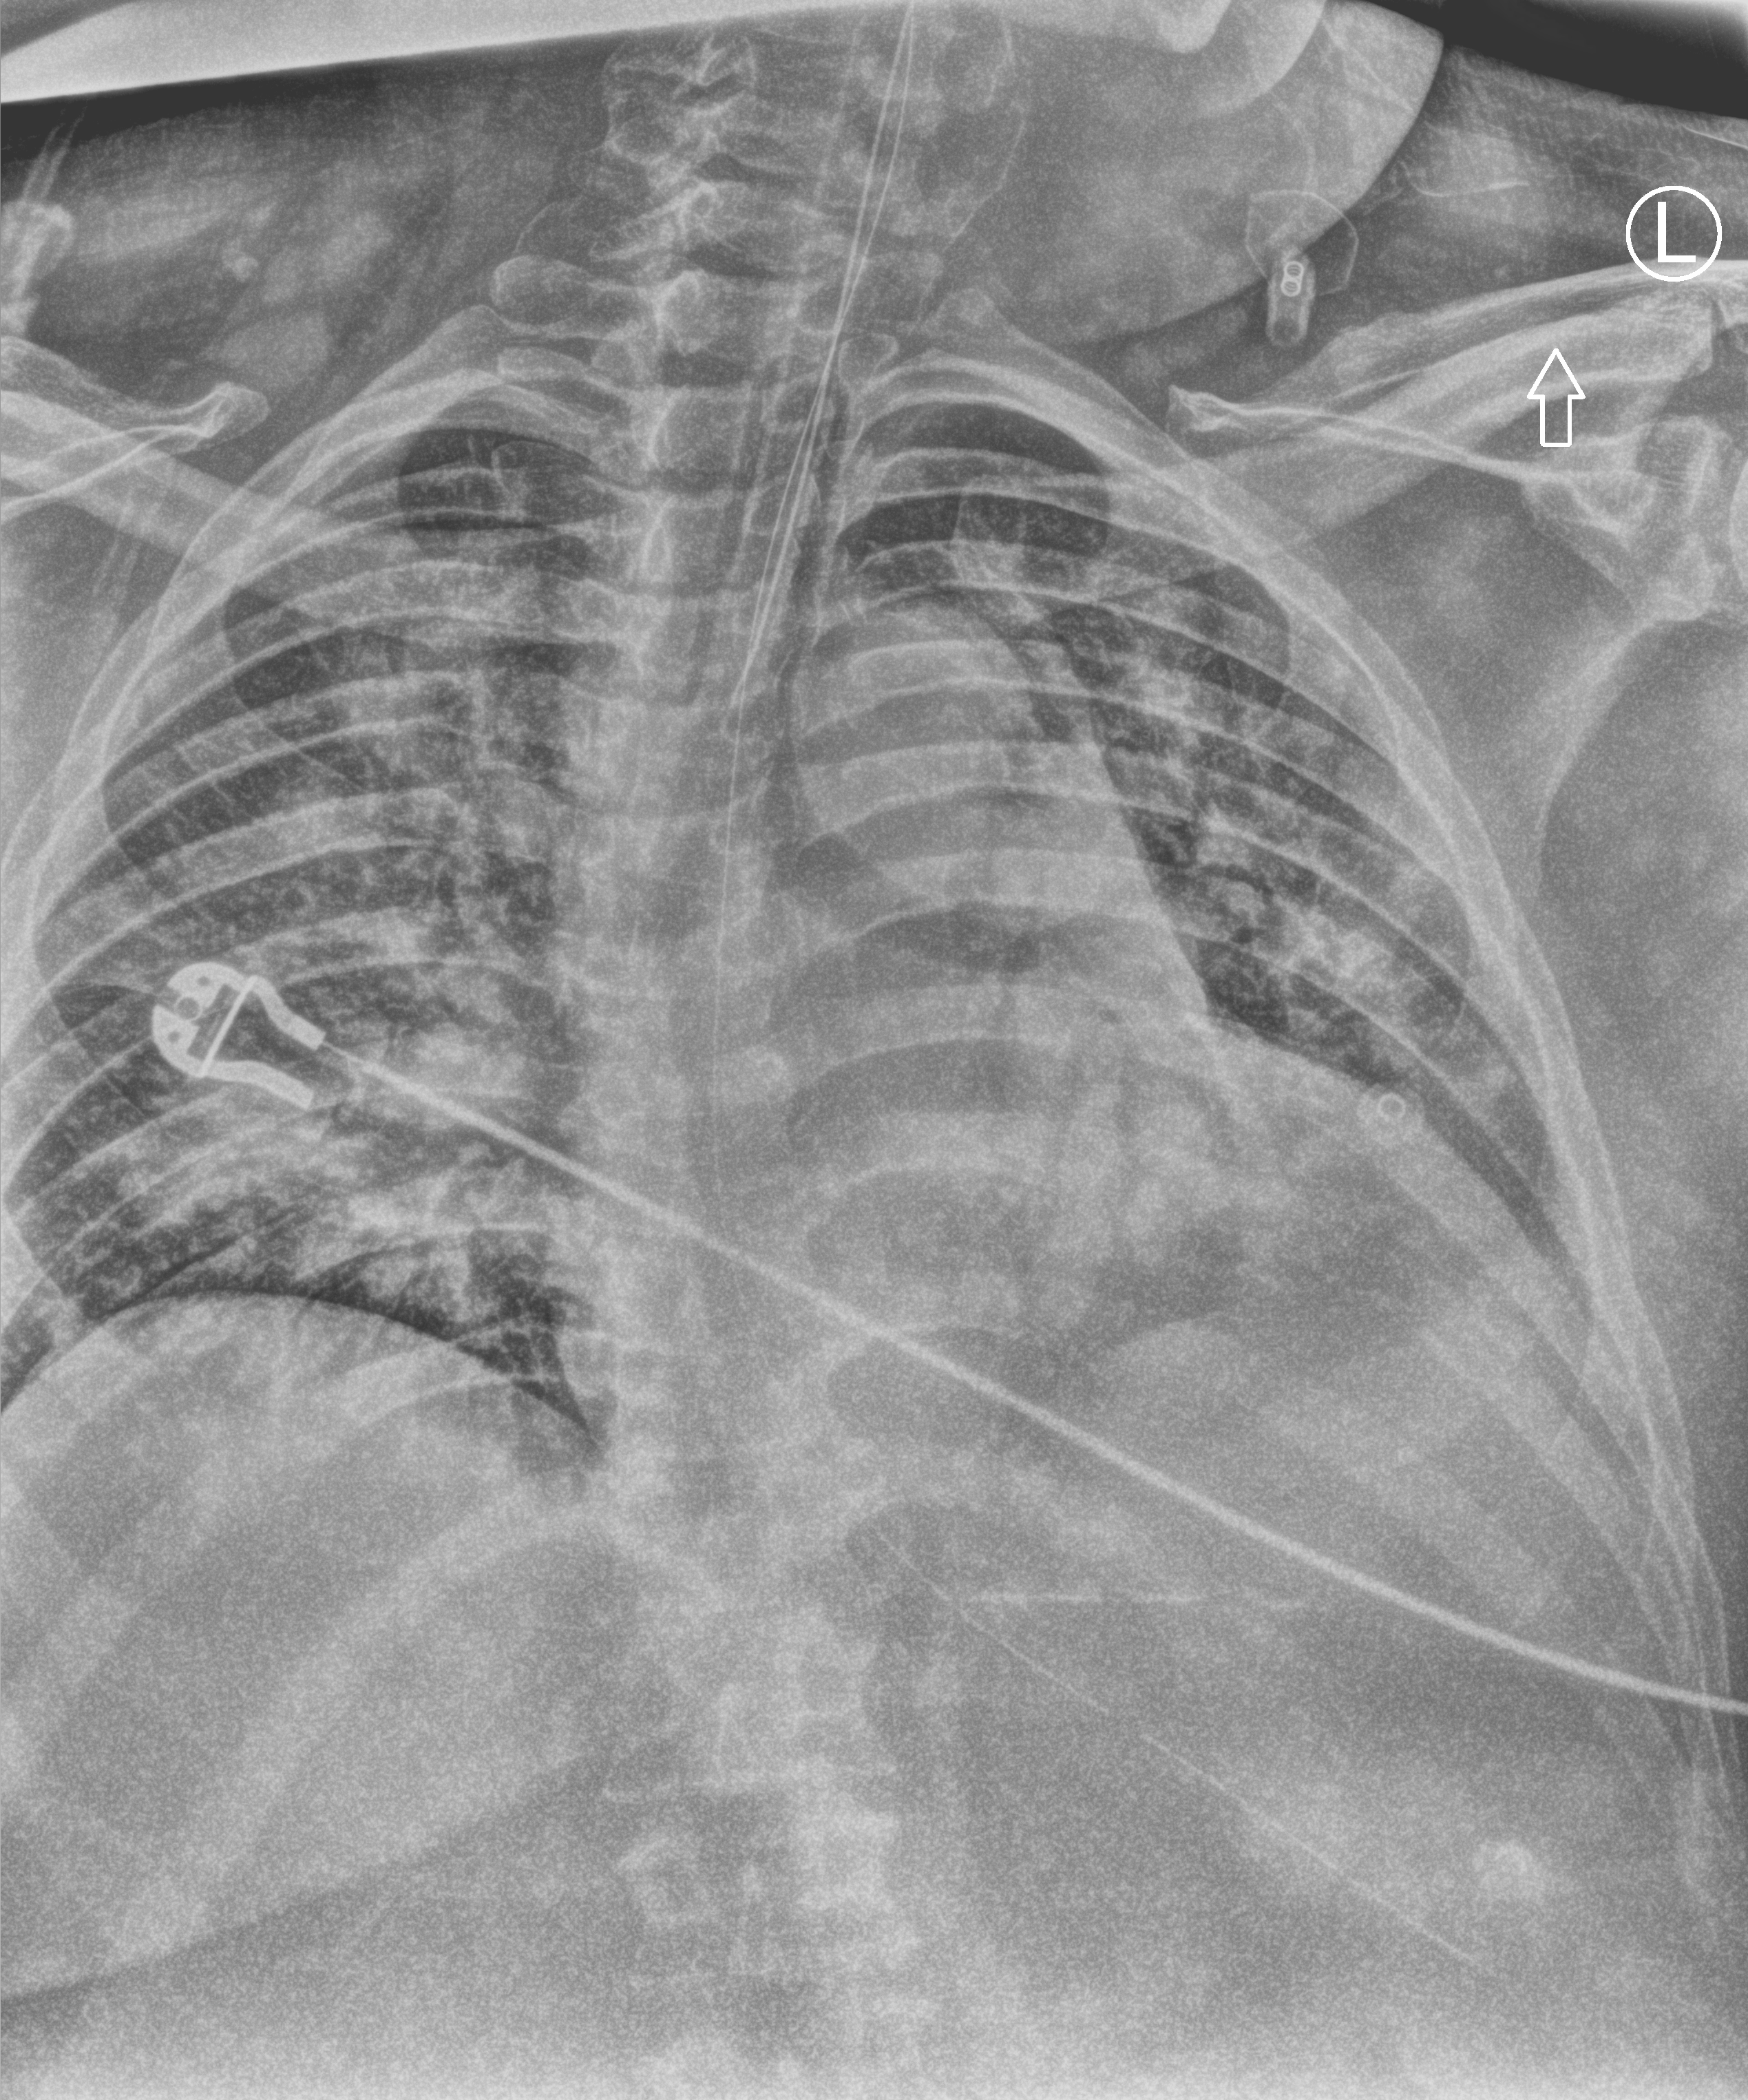
Chest X-ray (portable), anteroposterior (AP) projection. Male patient hospitalised with COVID-19, age 18–59 years.
From the hospital-stay record, not from the radiograph (when in the stay this image was taken is not recorded): mechanically ventilated during this hospital stay: yes; hypertension (admission record): no; admitted to intensive care during this hospital stay: yes.